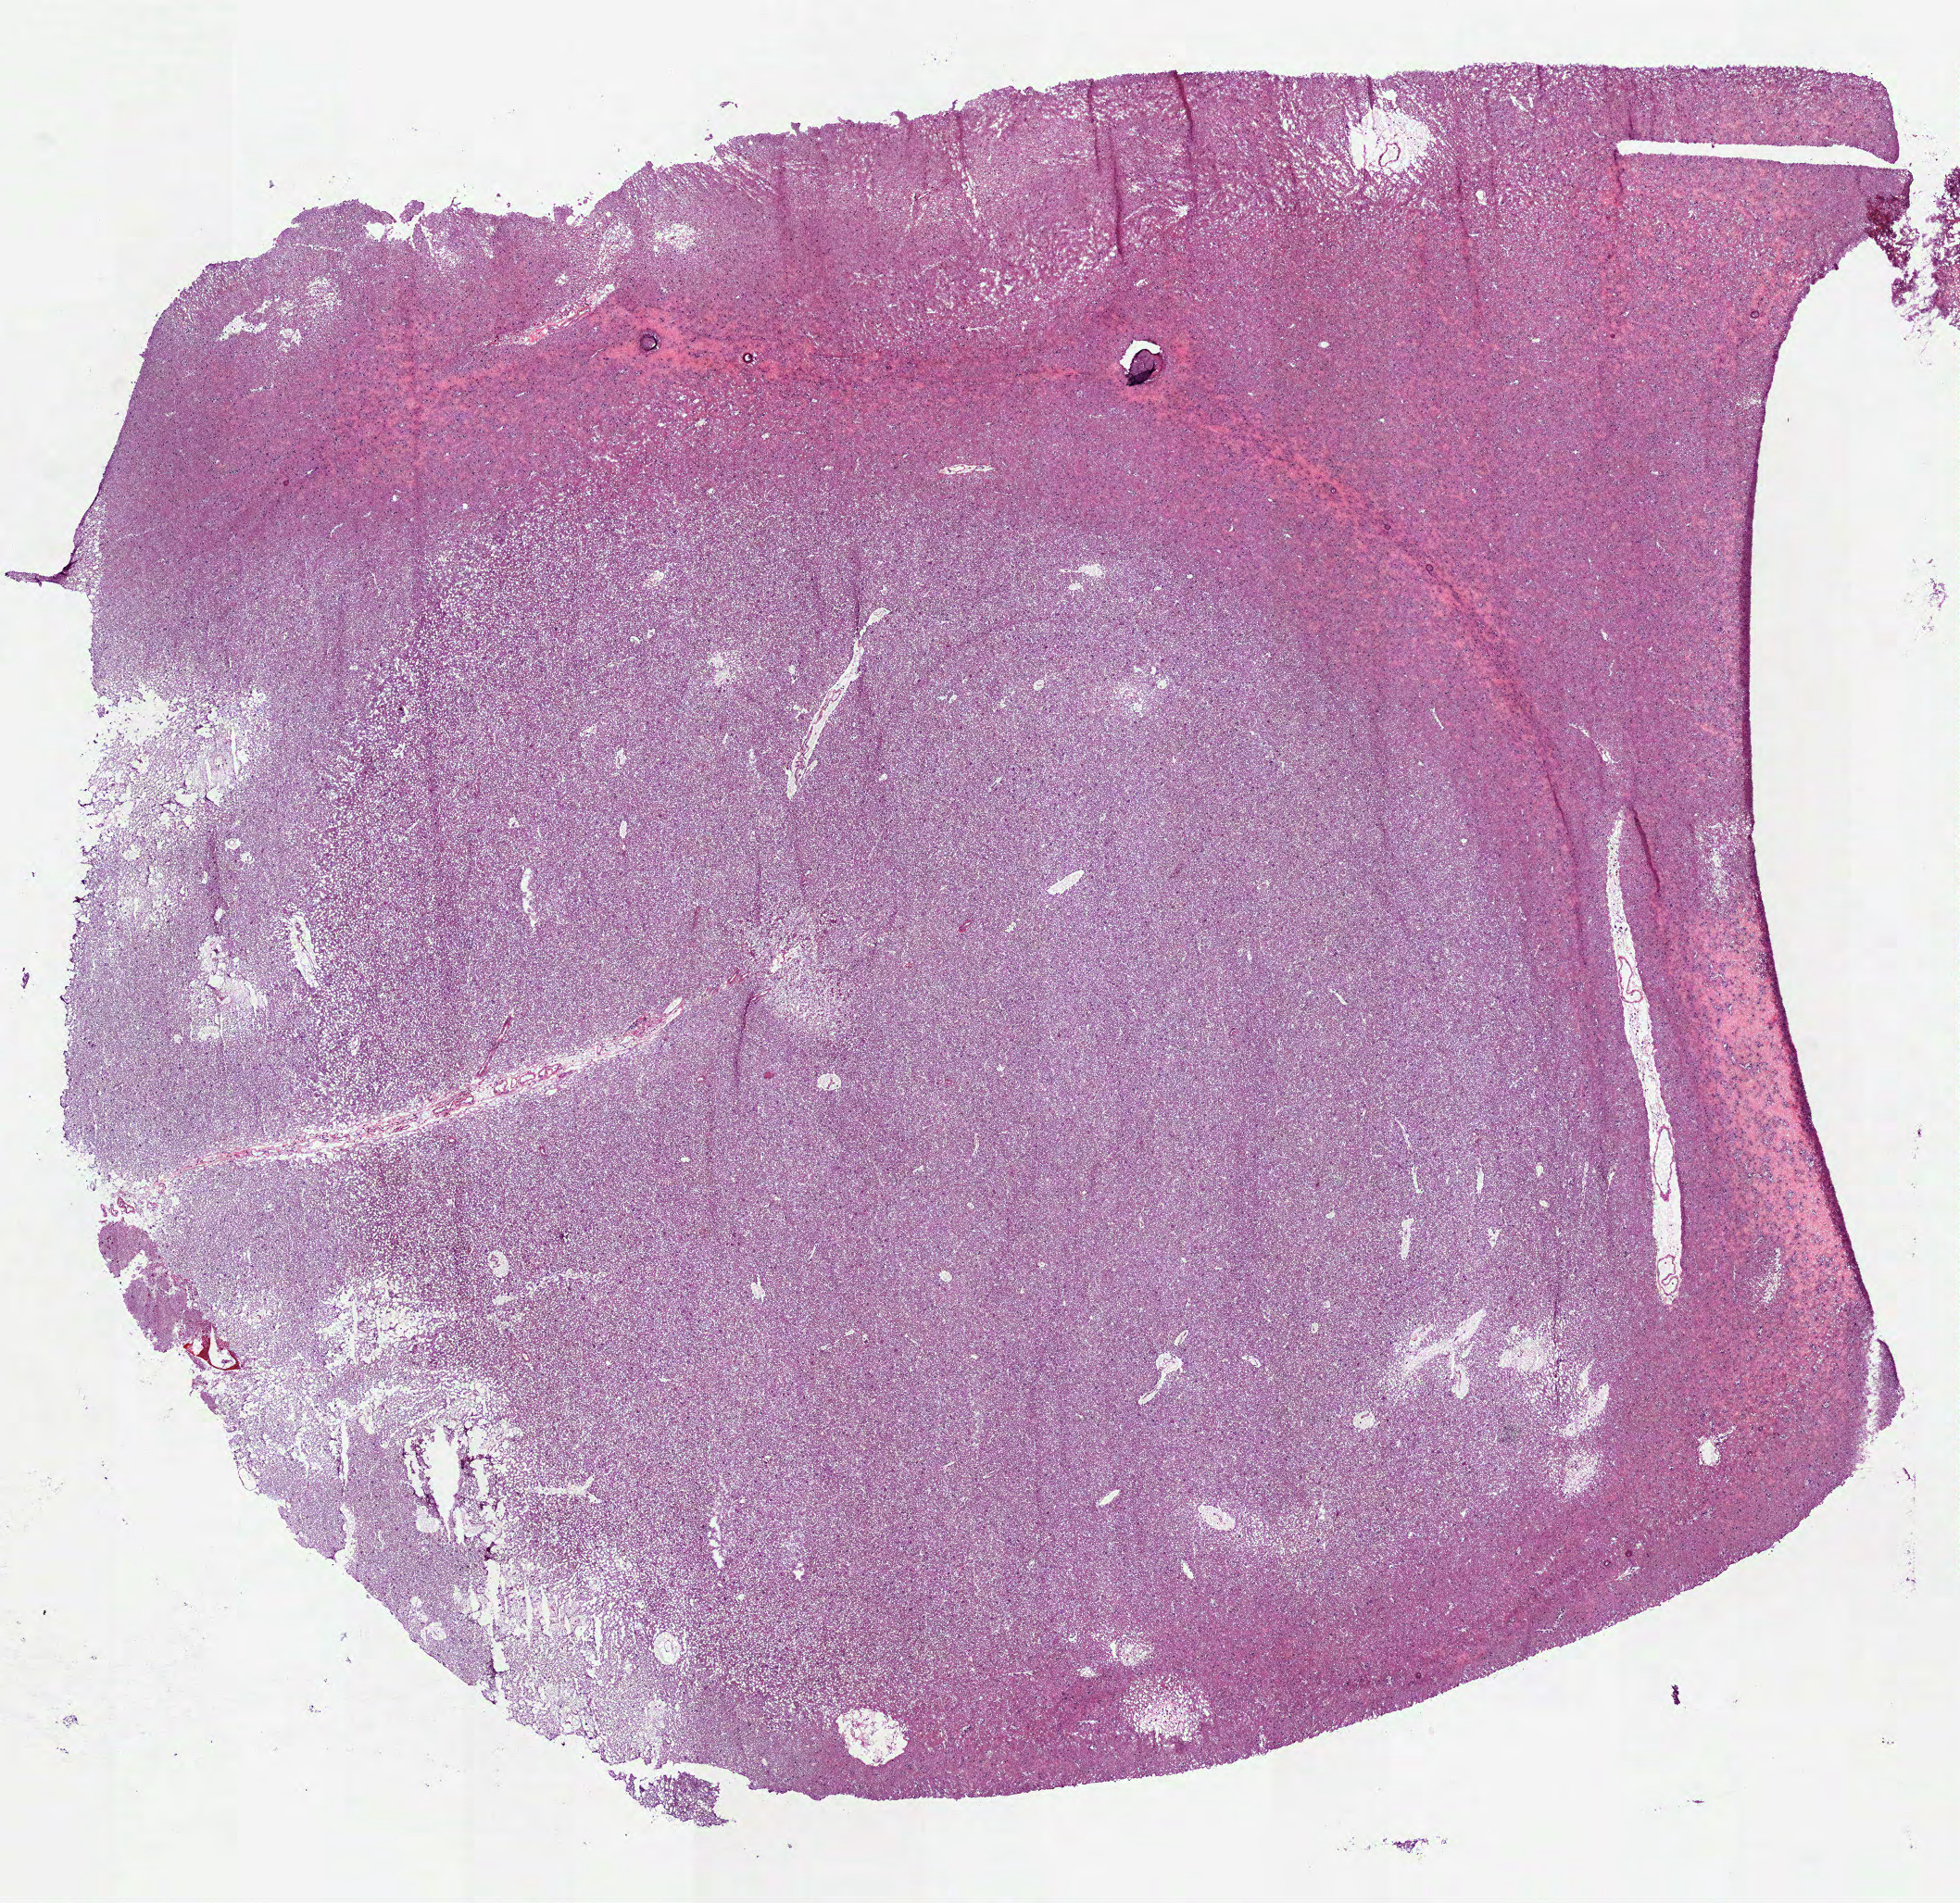
Hematoxylin and eosin (H&E) stained whole-slide image, low-resolution overview of the scanned area, about 8.5 x 8.3 mm (acquisition: 40x scan), frozen section, sample: primary tumour, brain. Female, age 29 years at initial diagnosis. Slide review estimates, as recorded: tumour cells 100%, tumour nuclei 60%.
Histologic diagnosis: Oligodendroglioma, NOS.